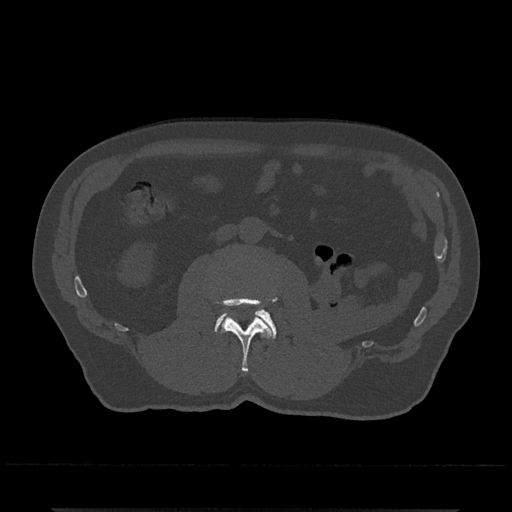
CT including the spine, one axial slice. Reconstruction kernel Br40s/3. Bone window (W 1800 / L 400 HU). 512 × 512 image matrix, field of view 393 × 393 mm. Patient: male, 67 years. Case-level facts recorded for this patient, not image findings: primary cancer: prostate.
Annotated regions visible in this slice (semi-automatic segmentation, software-assisted and operator-edited):
- L2 vertebra: box from (x=211, y=295) to (x=277, y=372) px
- L3 vertebra: (x=214, y=309)–(x=277, y=339)